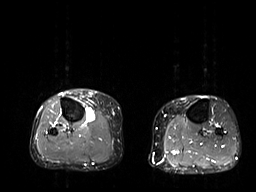
MRI of an extremity soft-tissue mass, one axial slice. Position 19 of 32 along the scan axis. STIR. 256 × 192 image matrix. Female patient. From the clinical record (not read from this slice): histological type: undifferentiated – high grade; grade: high; site of the primary tumour: right thigh.
Annotated regions visible in this slice (expert manual segmentation):
- gross tumour volume (mass): bounding box [x1, y1, x2, y2] px = [83, 107, 96, 122]